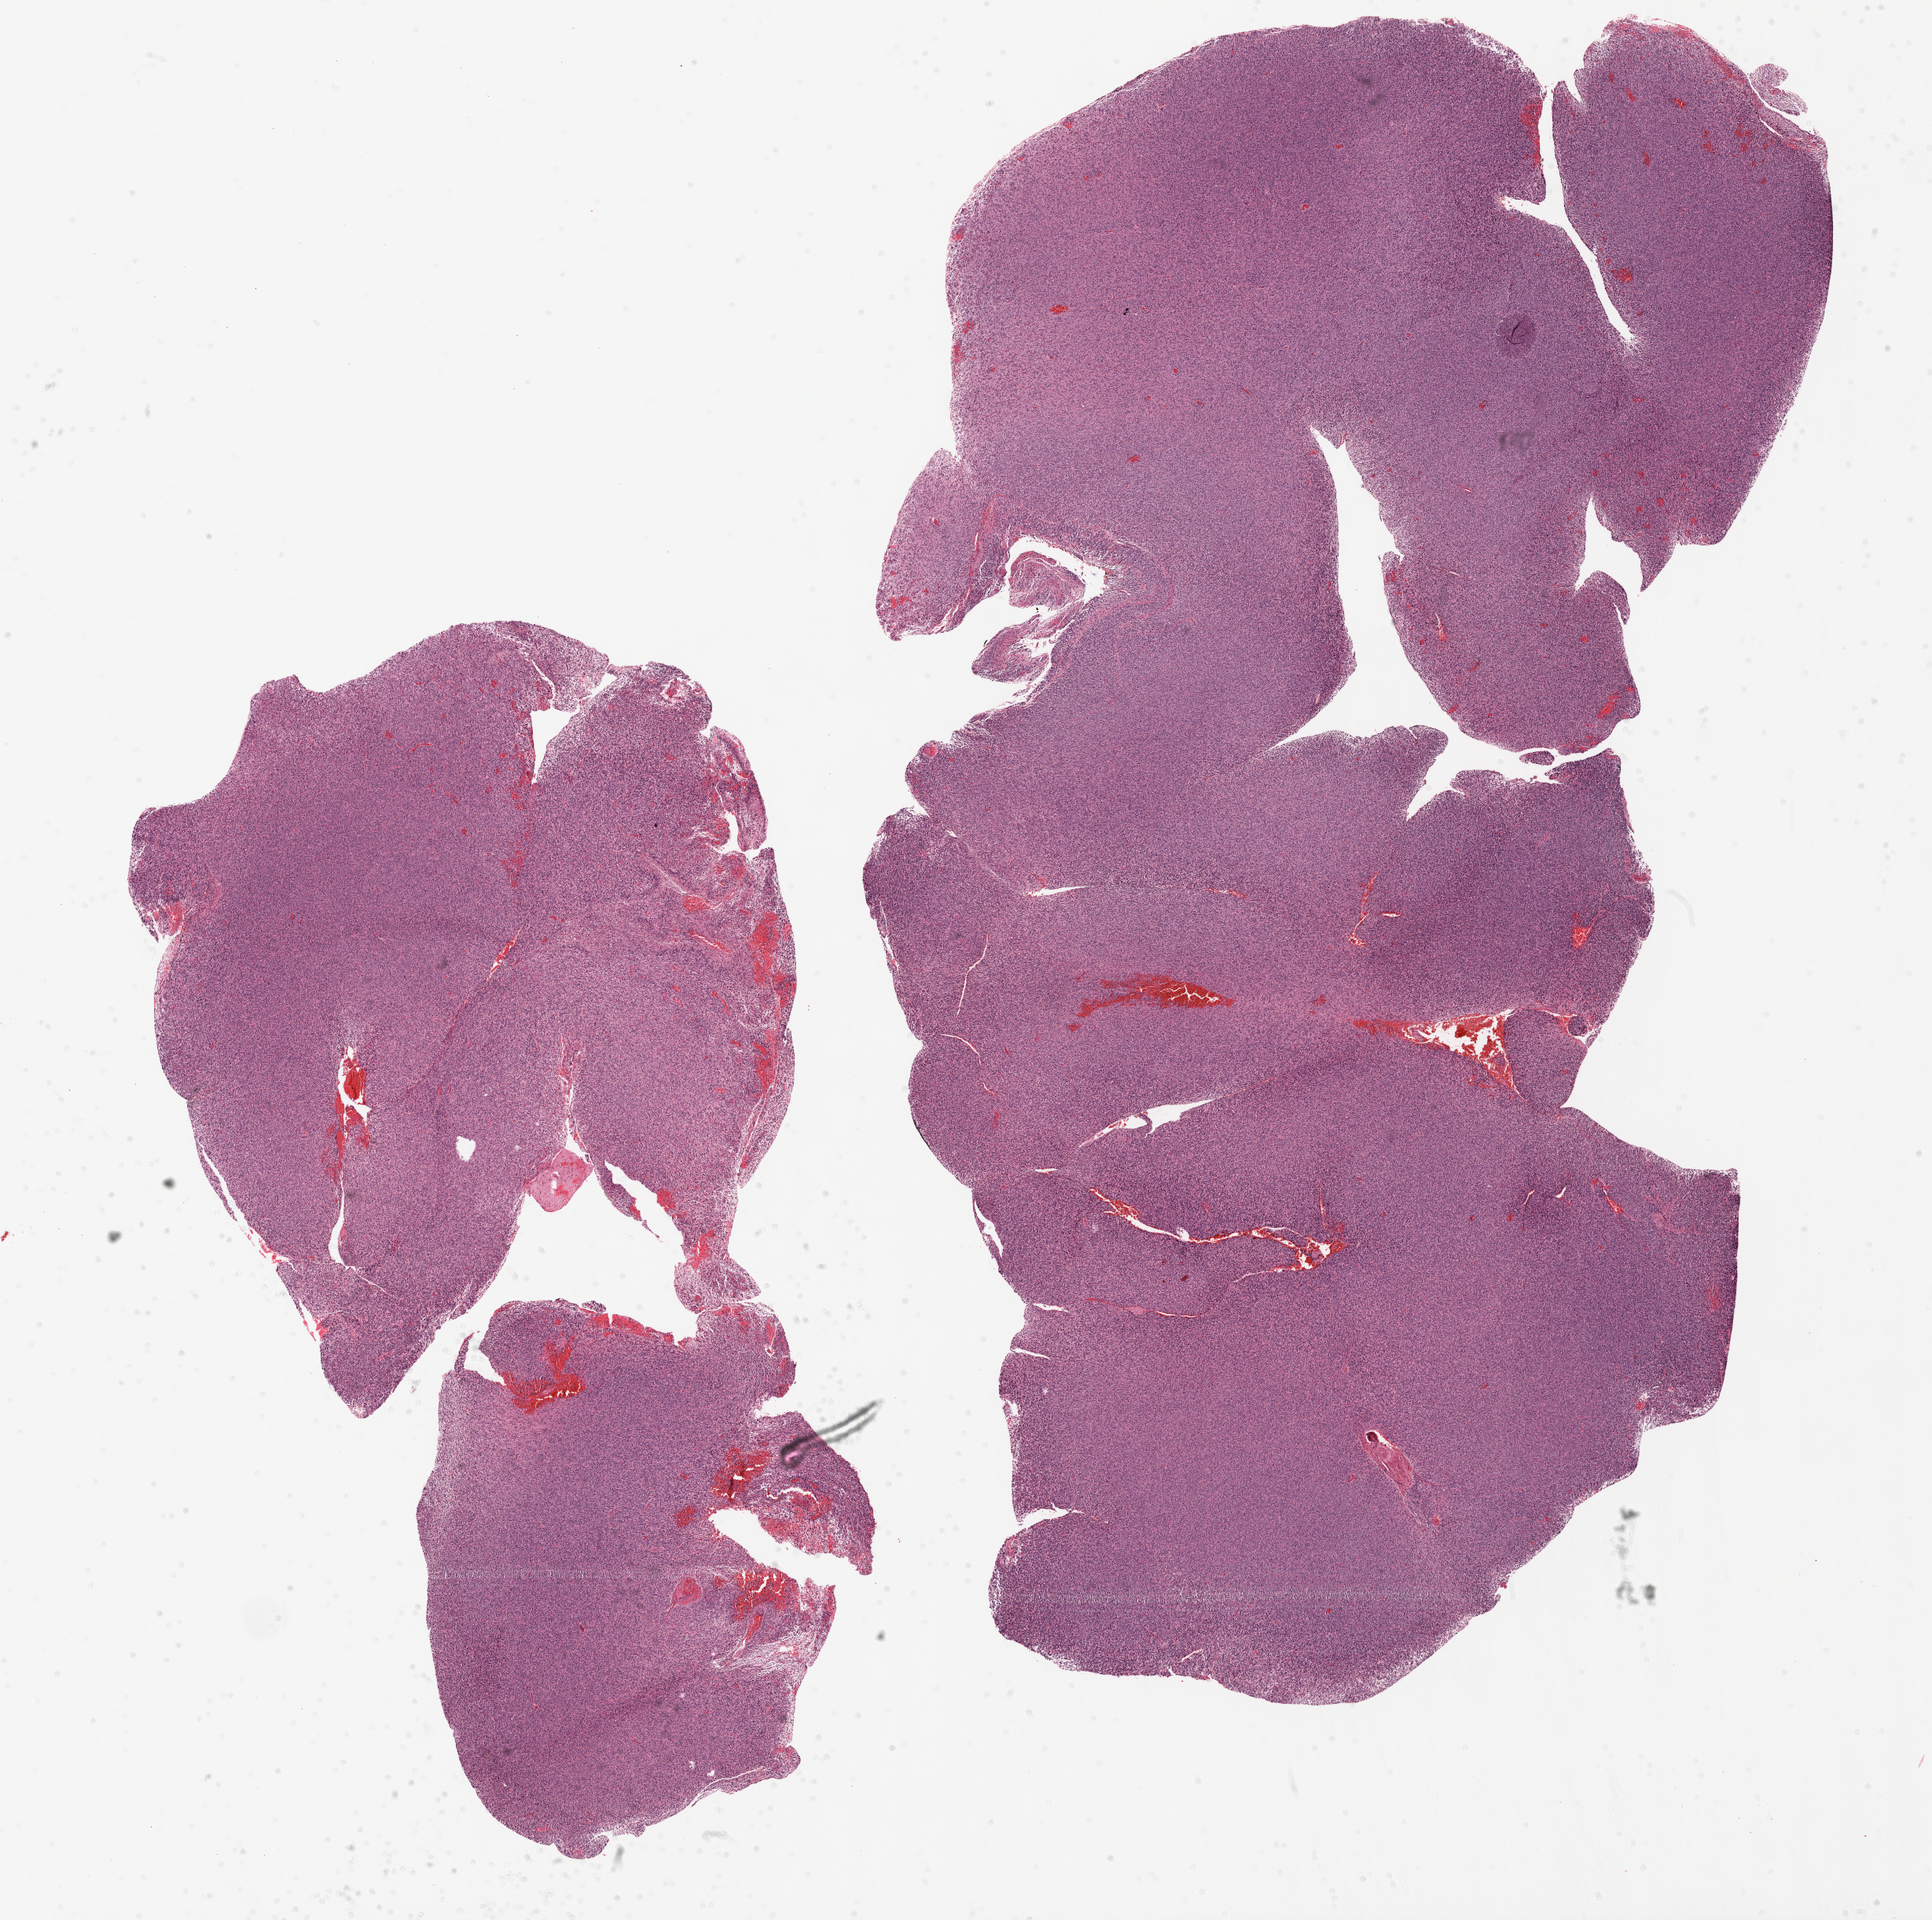
H&E-stained whole-slide image — low-resolution overview of the scanned area, about 19.8 x 19.7 mm; formalin-fixed paraffin-embedded (FFPE) diagnostic section; brain, primary tumour sample. Patient: male, age at initial diagnosis 65 years.
* diagnosis: Glioblastoma